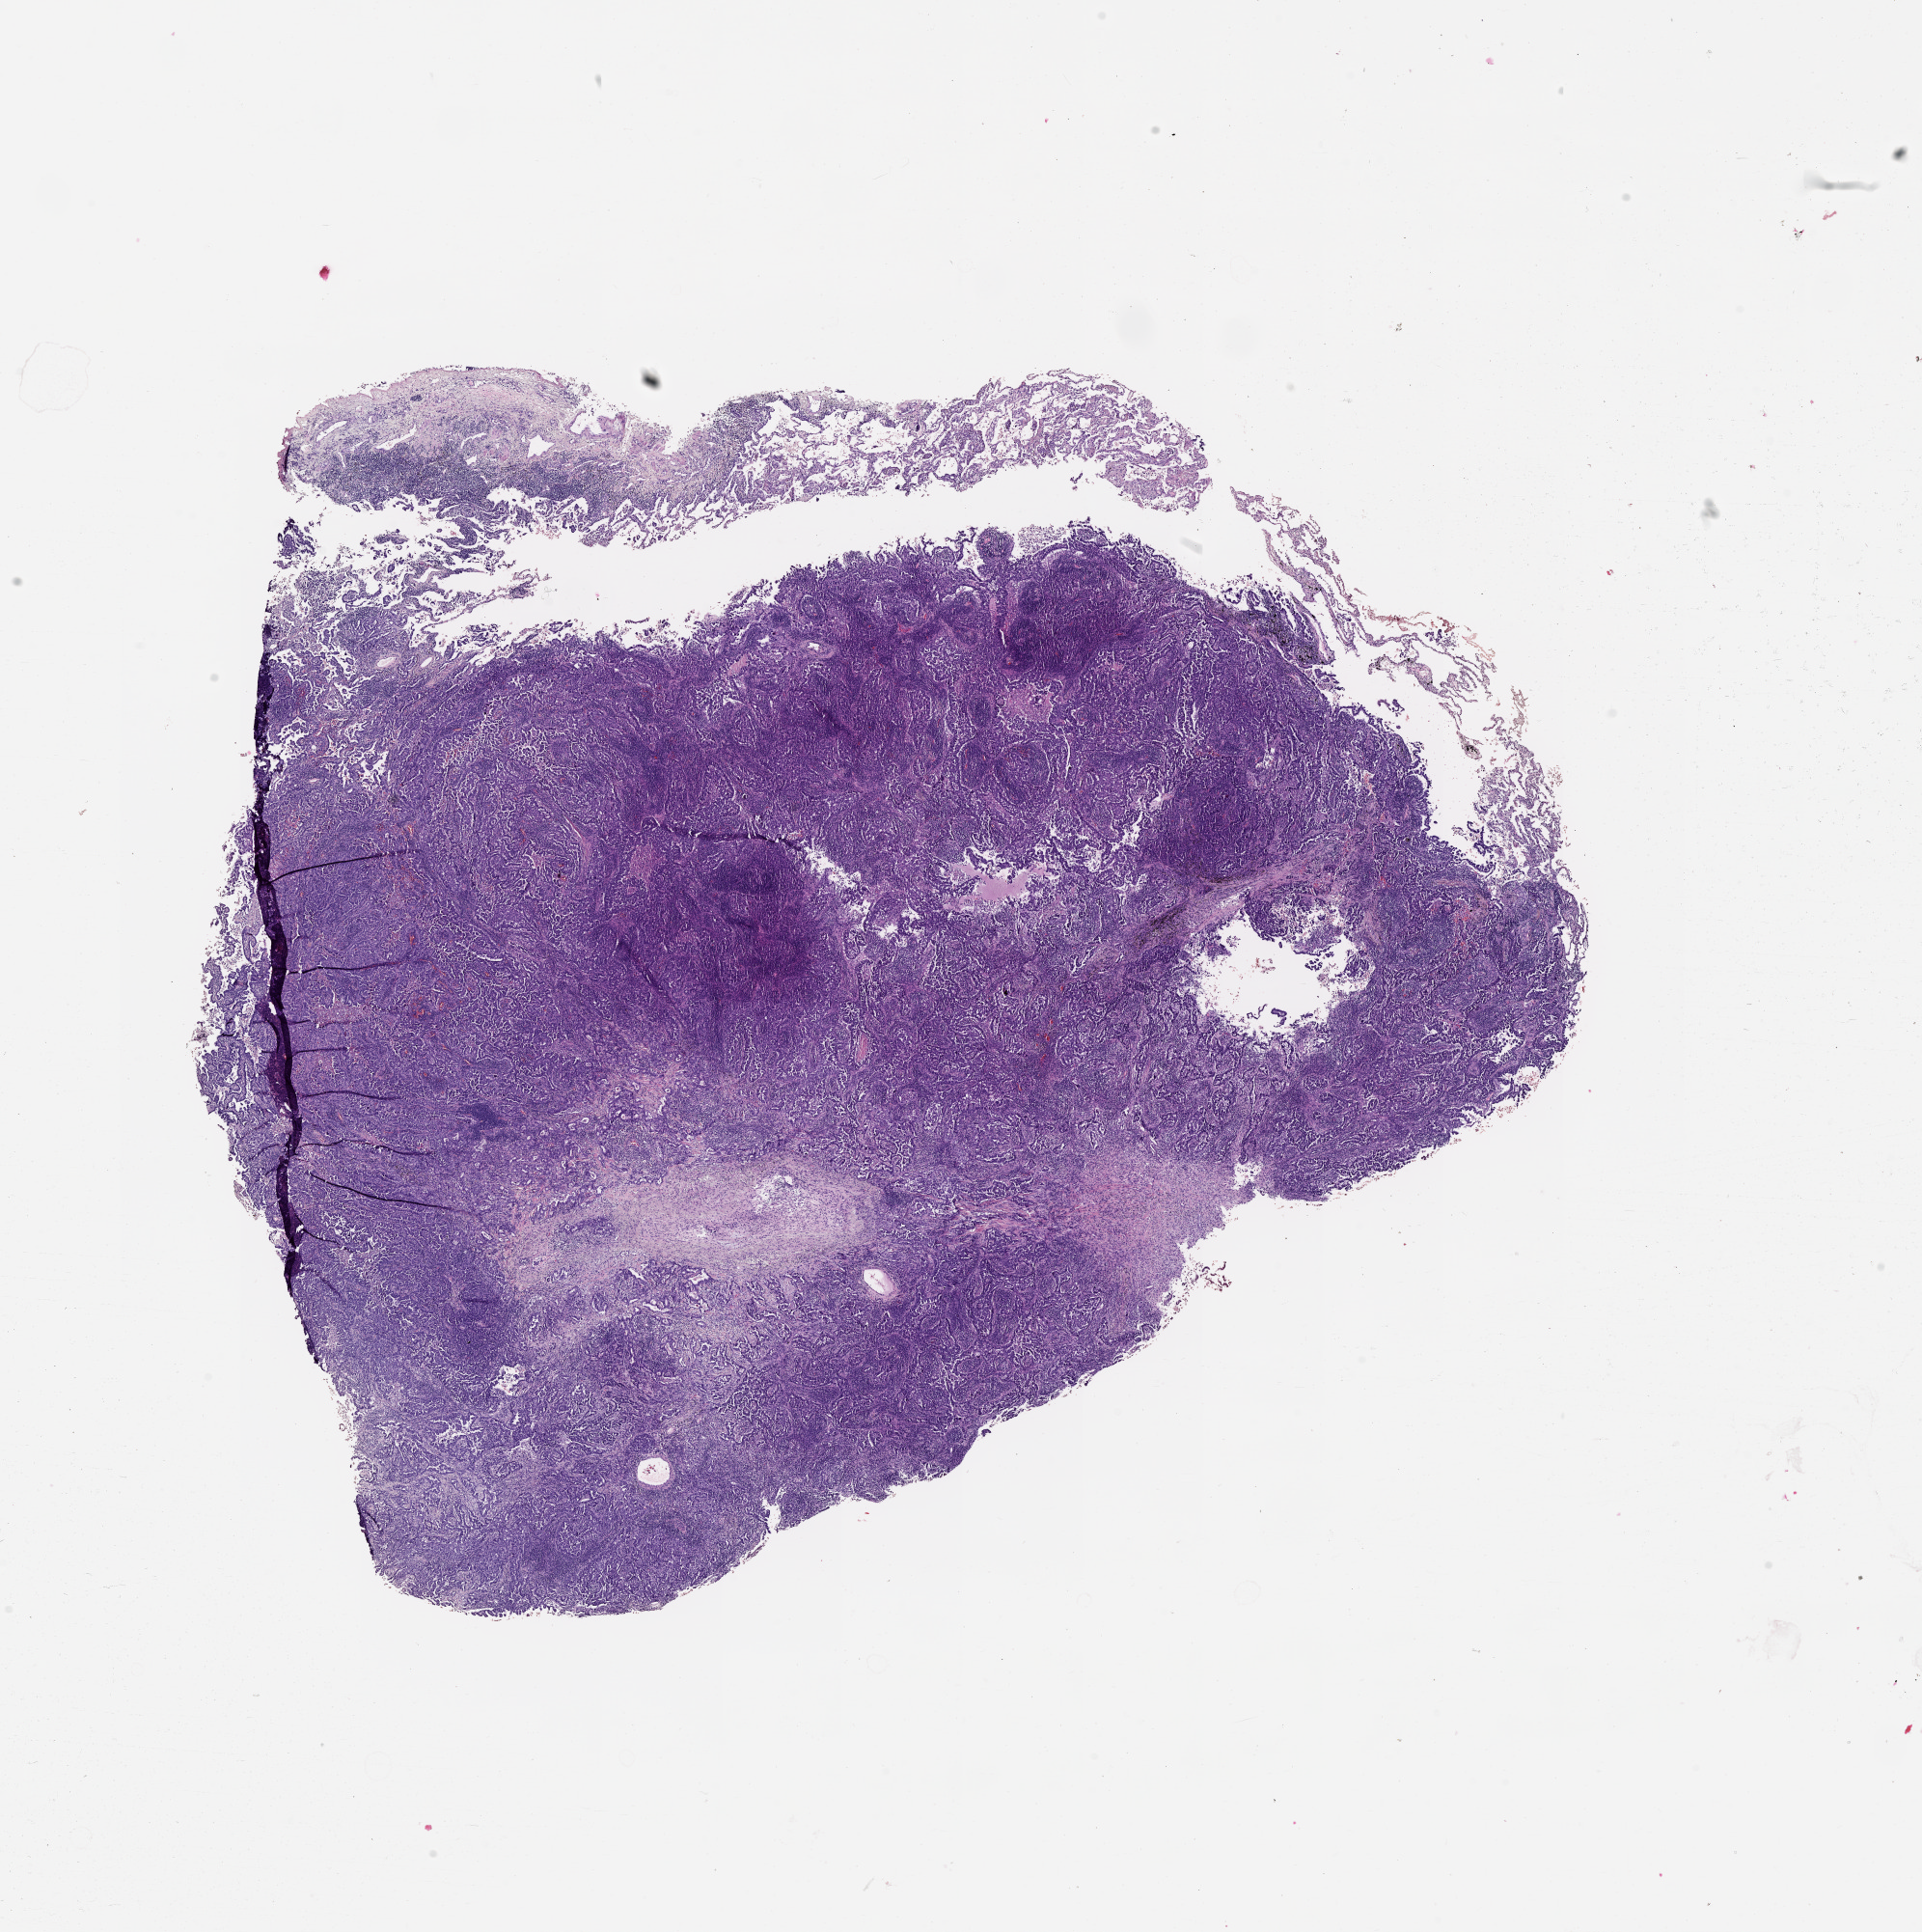
Digitized Hematoxylin and eosin (H&E) stained tissue section (whole slide), low-resolution overview of the scanned area, about 16.0 x 16.1 mm. Tumour tissue sample, lung. Patient: male, age 68 years.
Diagnosis: Adenocarcinoma, NOS.